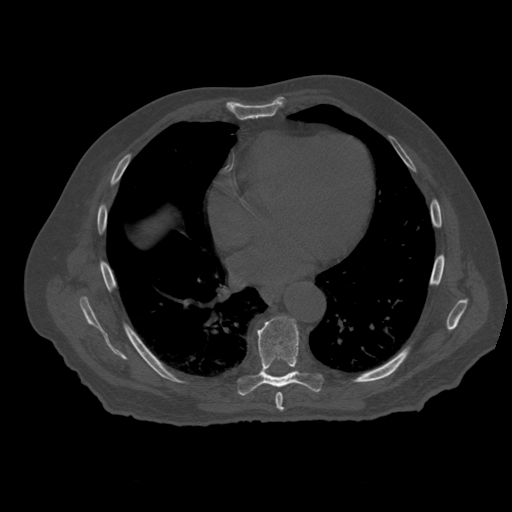
CT including the spine, one axial slice. Position 344 of 399 along the scan axis. Bone window (W 1800 / L 400 HU). 512 × 512 image matrix. Patient age 73 years. Case-level facts recorded for this patient, not image findings: primary cancer: prostate; vertebrae with lytic lesions (as recorded): L2.
Outlined on this slice (semi-automatically segmented with operator editing):
- T7 vertebra: bounding box [x1, y1, x2, y2] px = [276, 393, 284, 413]
- T8 vertebra: [238, 316, 324, 396]